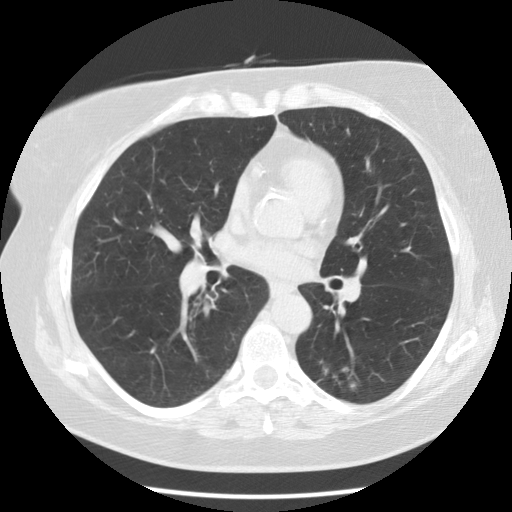
Axial slice from a low-dose chest CT screening exam, second screening round (one year after baseline), lung window (W 1500 / L -600 HU), 120 kVp, slice 58 of 118 in the series, 512 × 512 image matrix, field of view 340 × 340 mm. Female, age 59 years at enrolment.
Expert-annotated lung lesion, bounding box (x1, y1, x2, y2) in pixels: (294, 343, 374, 411). The screening reader recorded 5 non-calcified nodules or masses ≥4 mm on this exam (right upper lobe, right lower lobe, right lower lobe, left lower lobe, left lower lobe); which of them this box marks is not recorded. Official screen result: positive, other. Lung cancer was diagnosed 343 days after this screen: adenocarcinoma, NOS, left lower lobe, poorly differentiated (G3), stage IA (AJCC 6th edition), 15 mm at pathology.